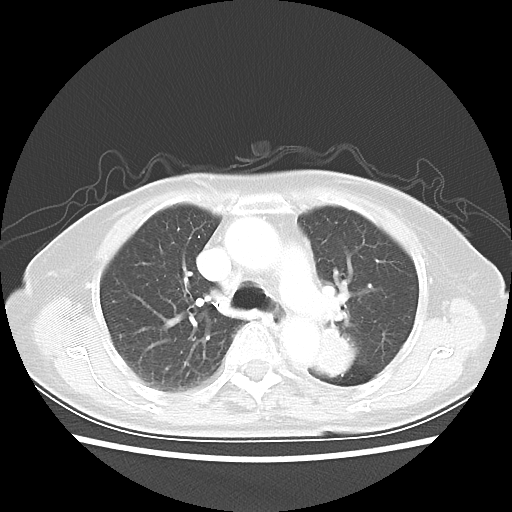
Chest CT, one axial slice; slice 33 of 50 in the series (ordered by position); reconstruction kernel LUNG; lung window (W 1500 / L -600 HU); 5 mm slice thickness; 512 × 512 image matrix. Patient: female, 81 years. Case-level facts recorded for this patient, not image findings: clinical TNM (as recorded): T2 N0 M1a.
Annotated regions visible in this slice (bounding box drawn by a radiologist):
- lung tumour (recorded histology: squamous cell carcinoma): bounding box [x1, y1, x2, y2] px = [311, 321, 363, 385]